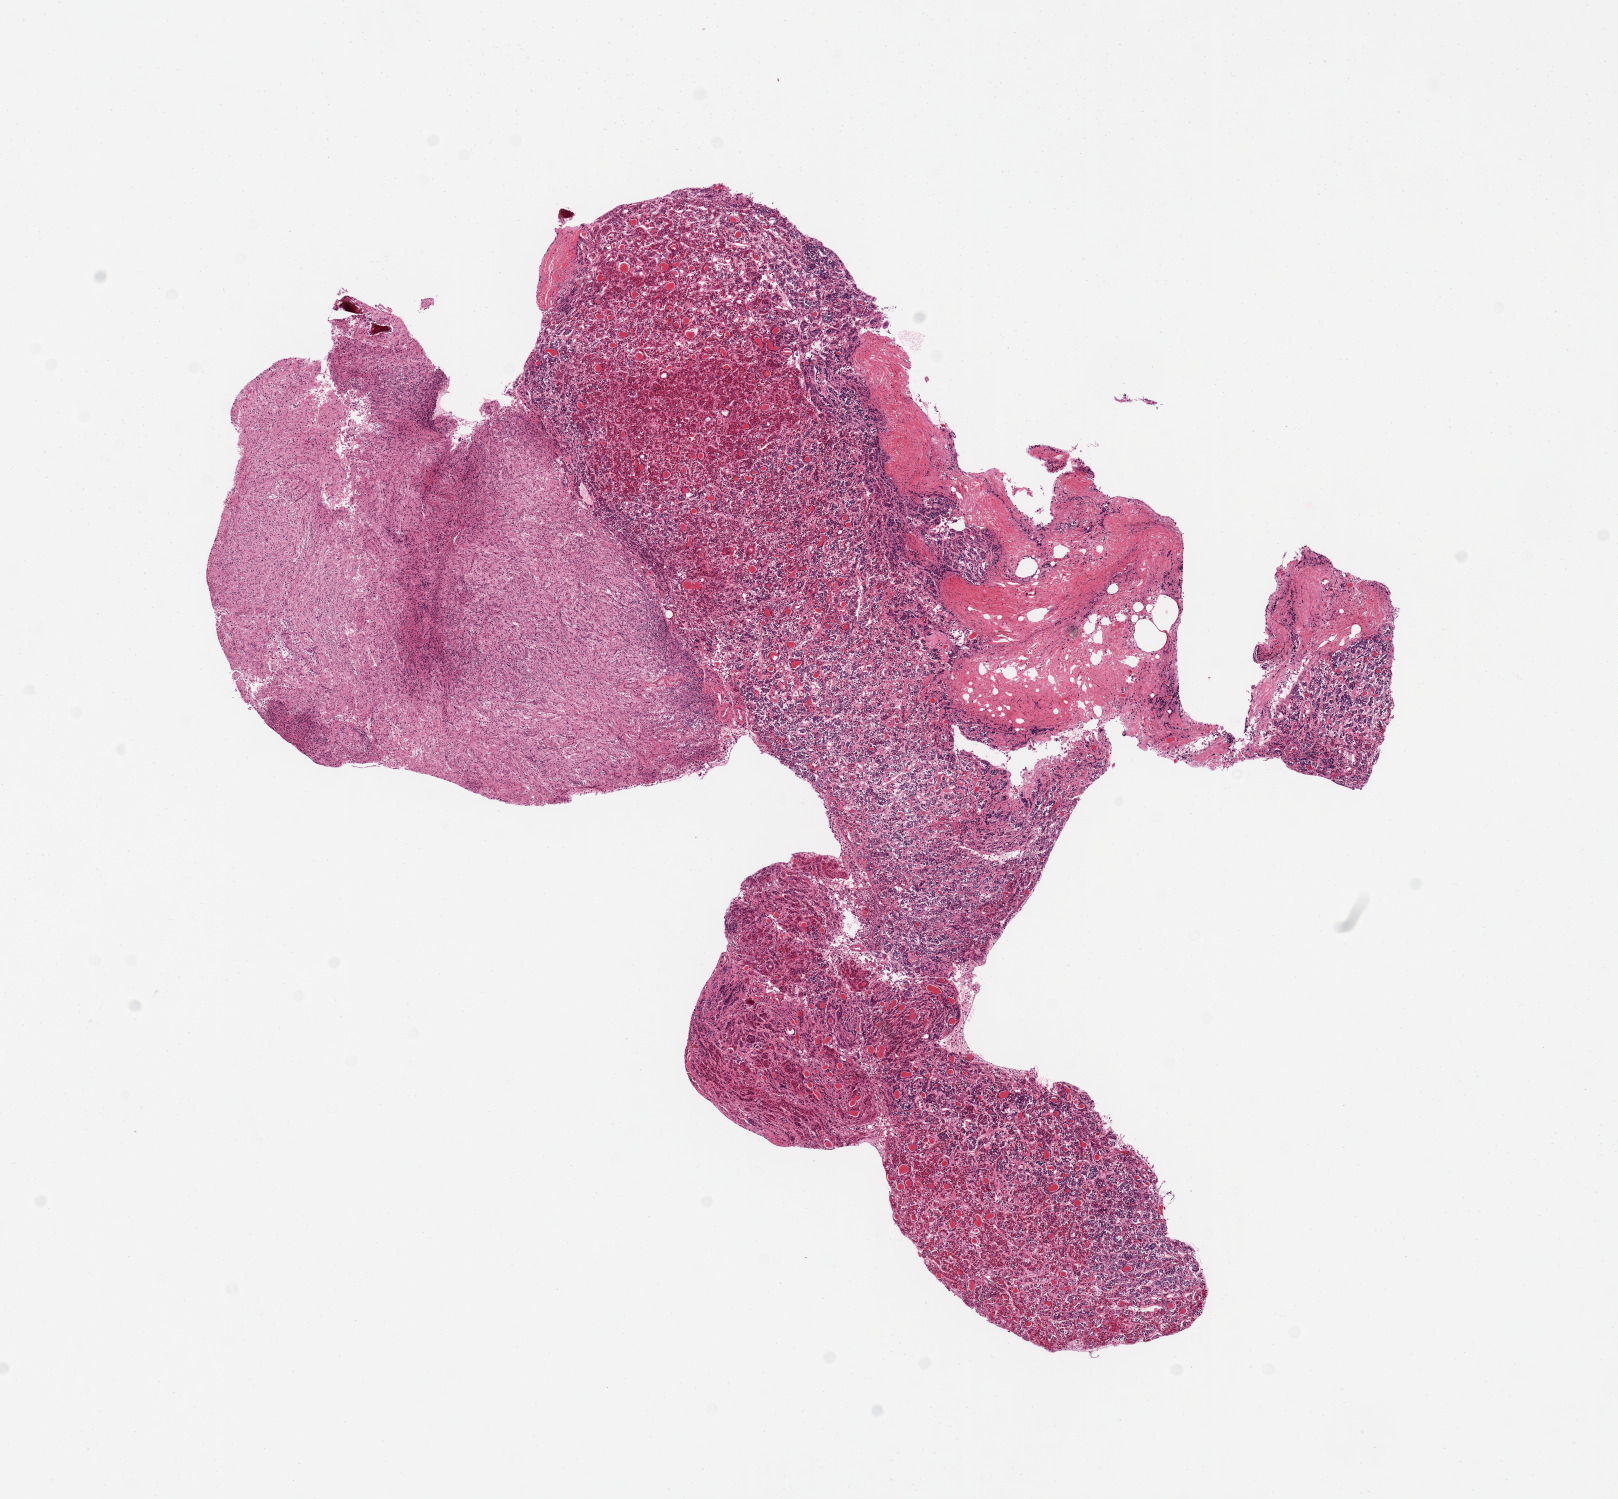
Digitized hematoxylin and eosin (H&E)-stained section — whole scanned area (about 12.8 x 11.9 mm, acquisition: 20x scan) shown as a low-resolution overview; PAXgene-fixed, paraffin-embedded tissue; target tissue: pituitary; donor tissue sample.
- reviewer comment on this tissue sample: 1 piece with anterior and posterior portions